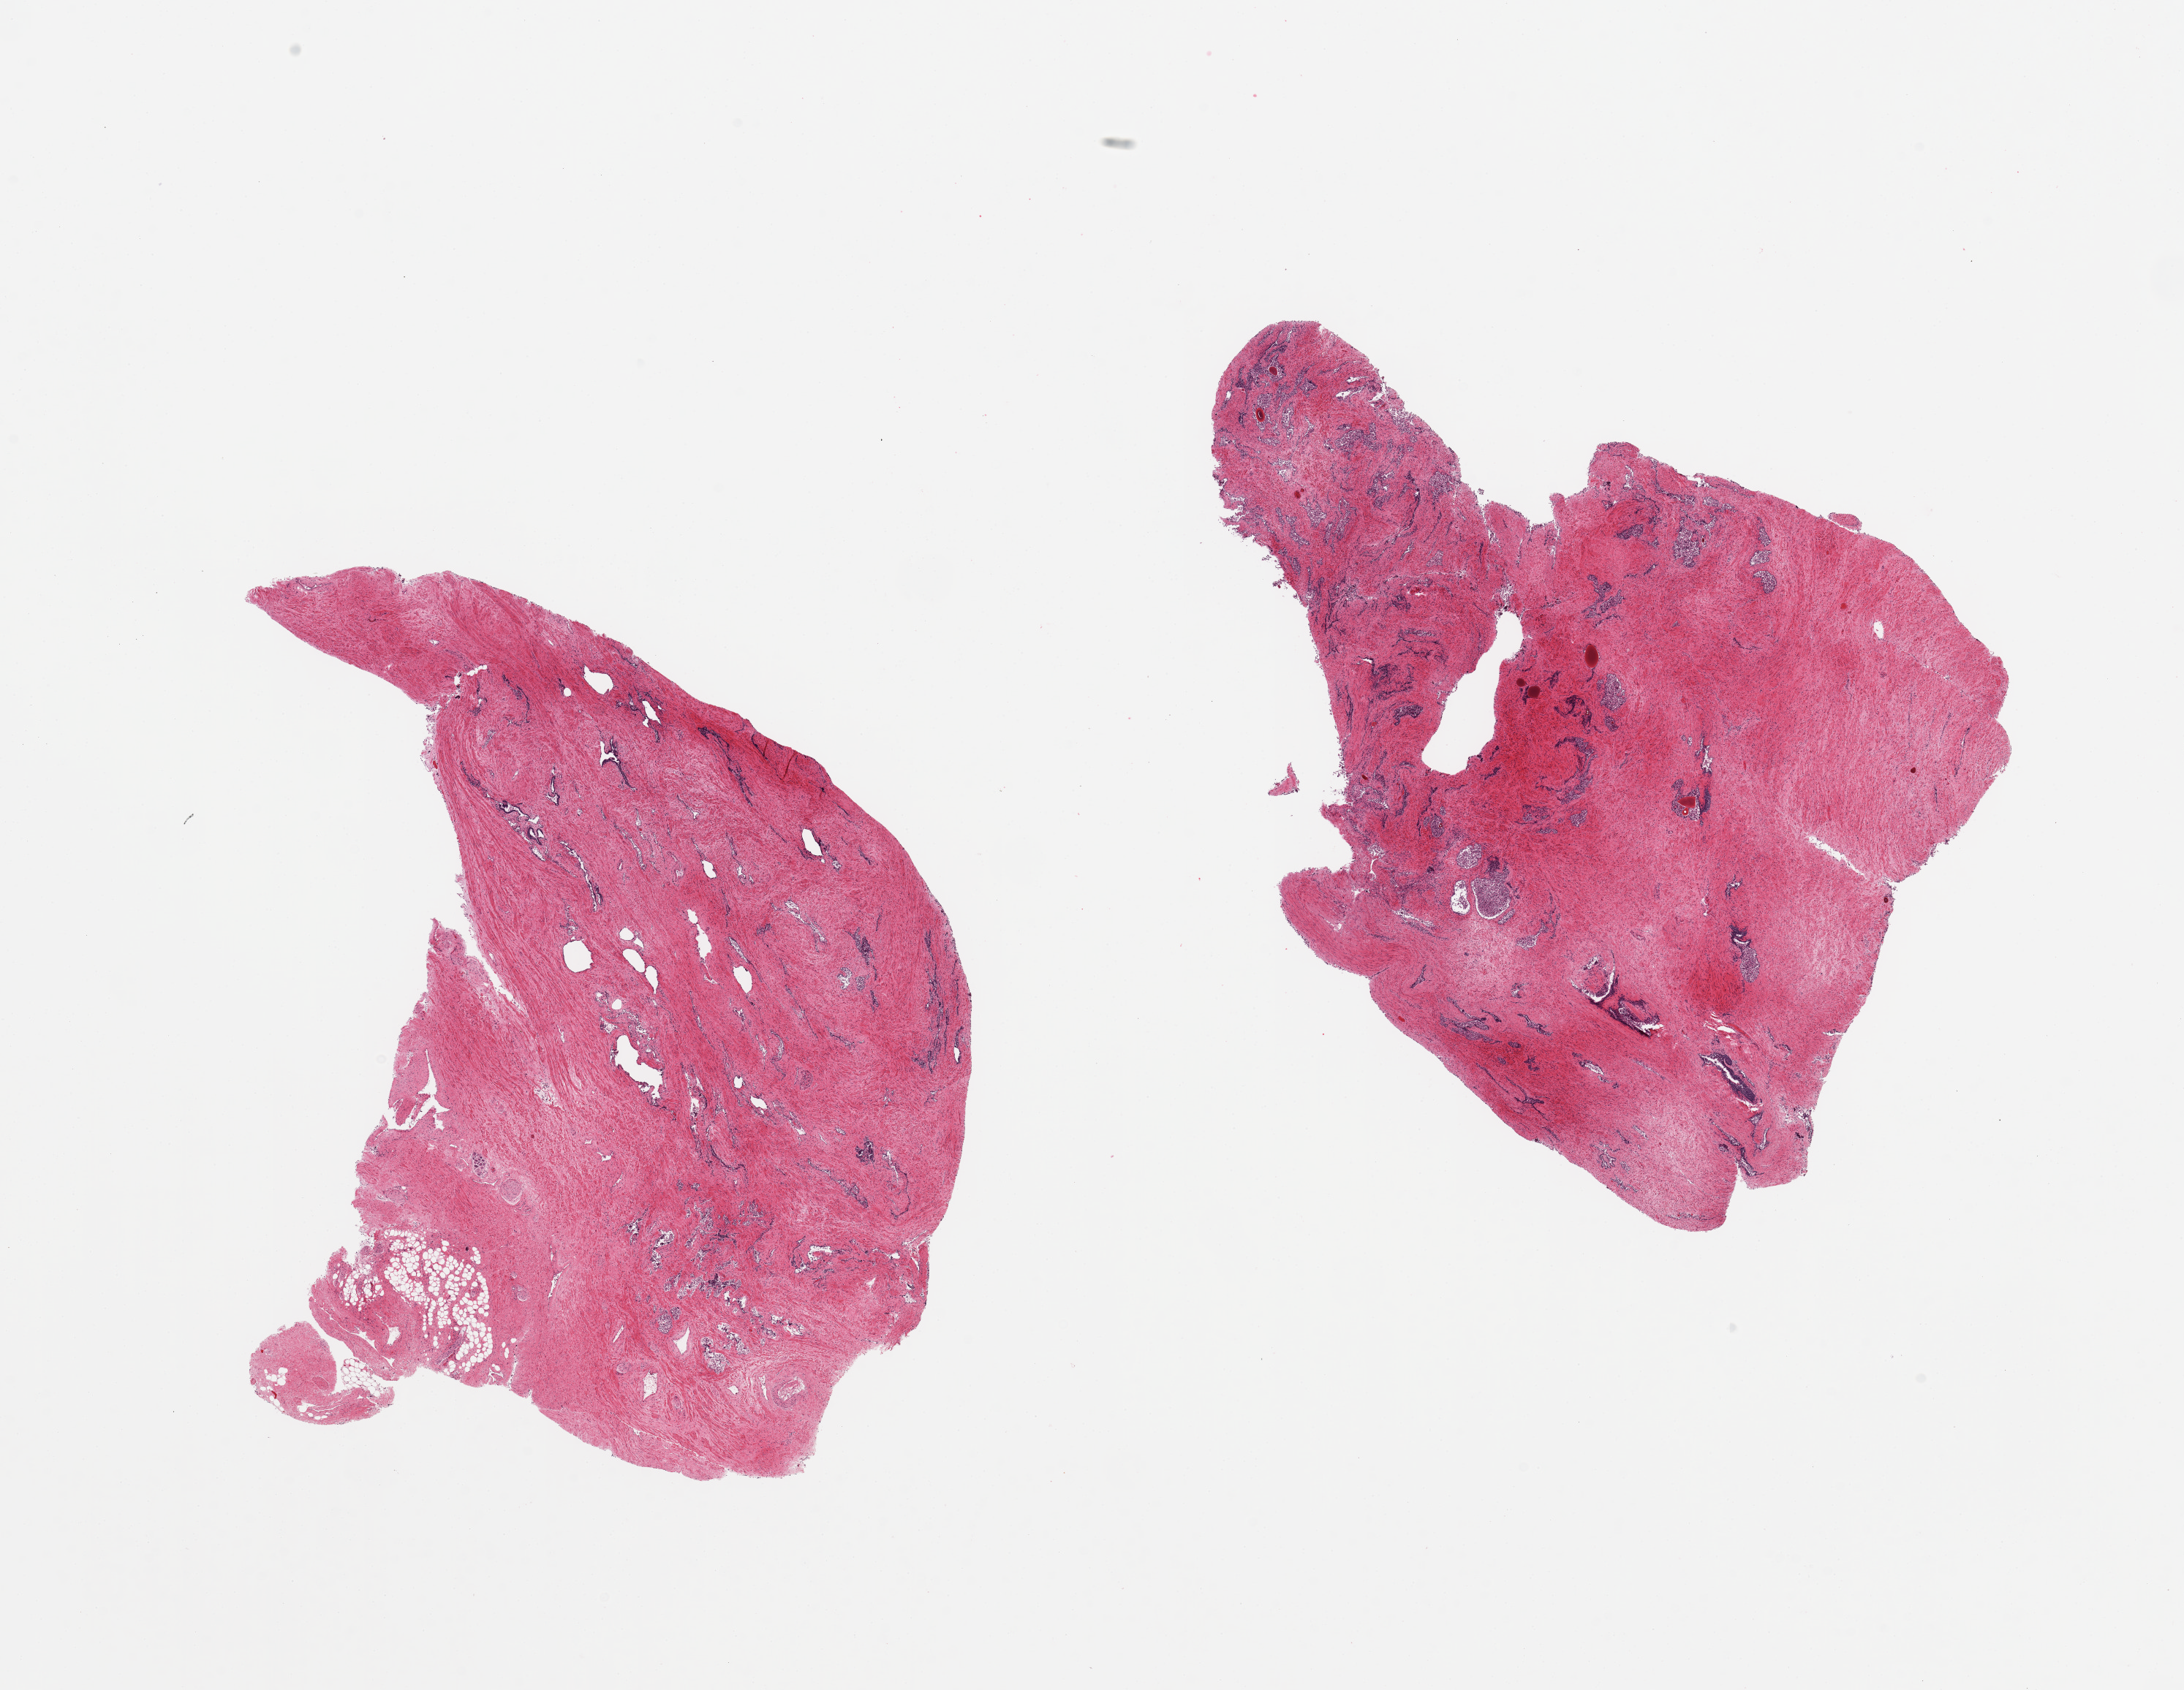
Whole-slide image, H&E stain, brightfield — a low-resolution overview of the entire scanned area, about 23.6 x 18.3 mm, PAXgene-fixed paraffin-embedded (PFPE) section, section of prostate (target tissue), donor tissue sample.
• review note (as recorded): 2 pieces; fibromuscular stroma and embedded glands with sloughed epithelium, minimnal fat and nerve